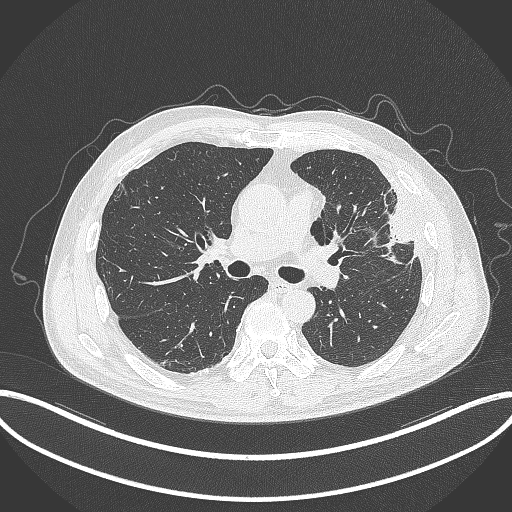
Chest CT, one axial slice. Slice 198 of 382 in the series (ordered by position). Reconstruction kernel B70f. Lung window (W 1500 / L -600 HU). 1 mm slice thickness. 512 × 512 image matrix. Male patient, age 64 years. From the clinical record (not read from this slice): clinical TNM (as recorded): T4 N1 M0; histopathological grade: G3.
Structures marked on this image (rectangle marked by the reading radiologist):
- lung tumour (recorded histology: adenocarcinoma): box from (x=380, y=193) to (x=422, y=263) px